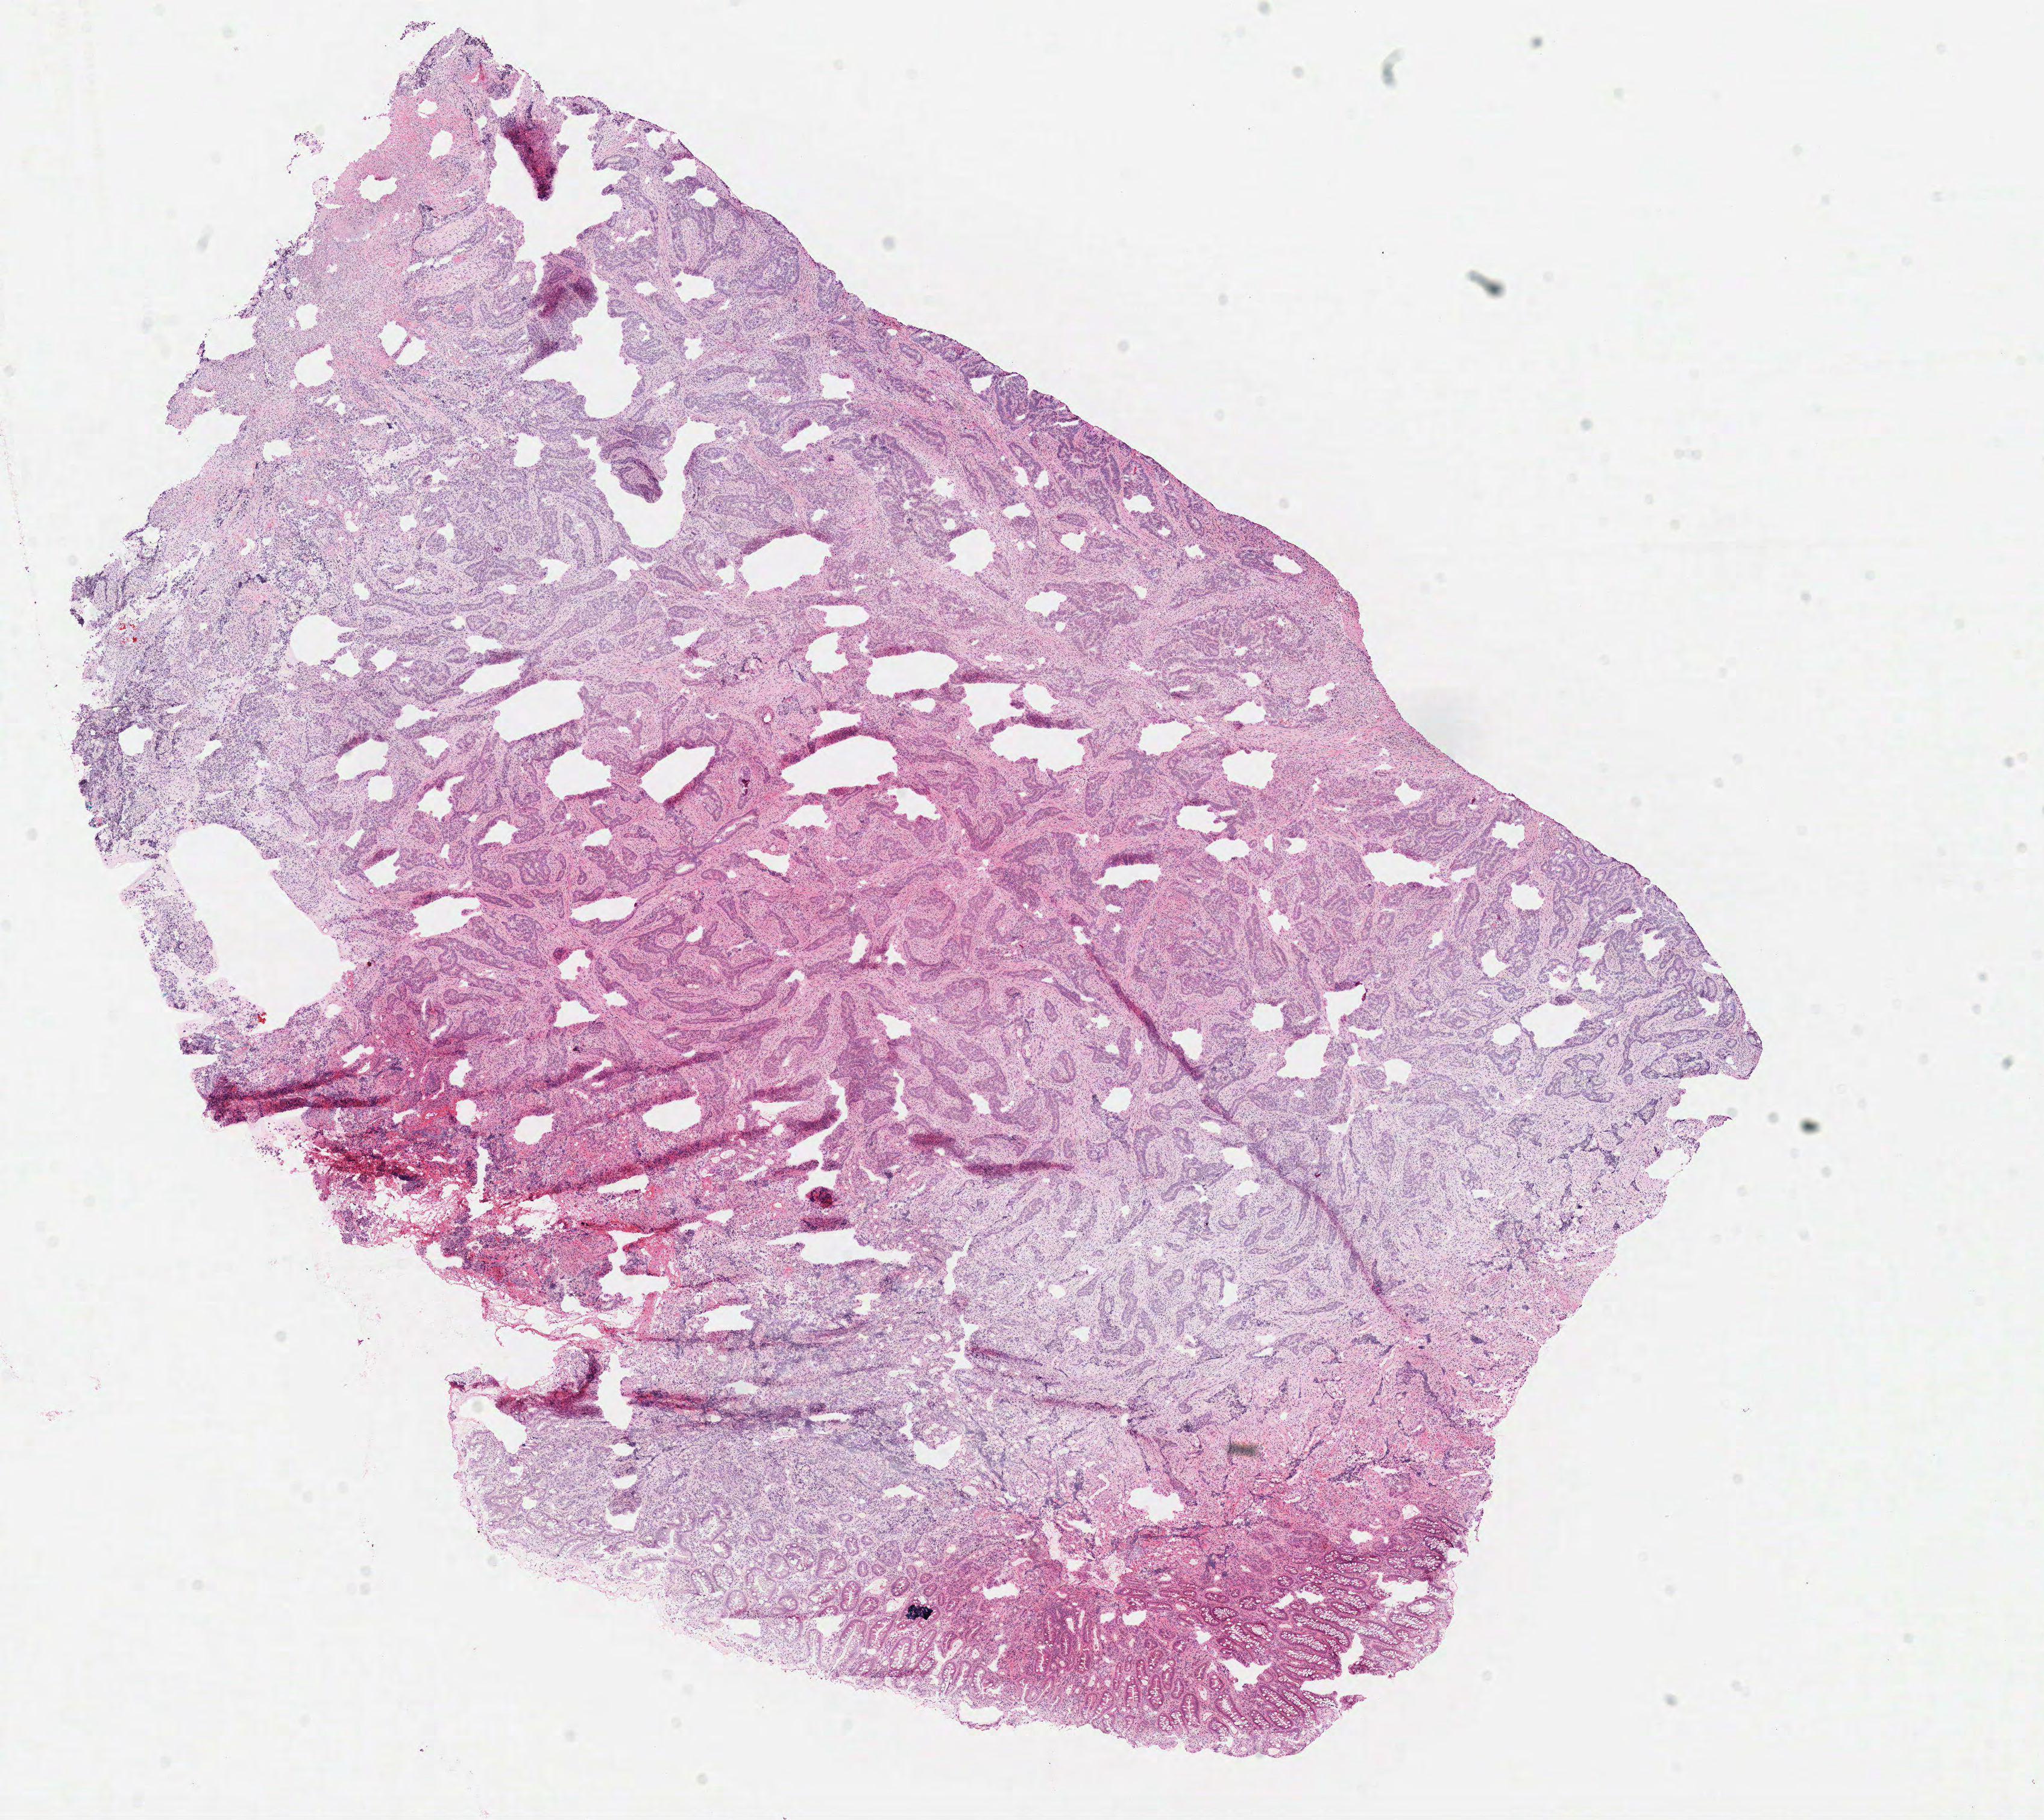
H&E whole-slide image — whole scanned area (about 13.4 x 11.9 mm) shown as a low-resolution overview; frozen section from the top of the tissue portion; rectum, primary tumour sample. Patient: male, age at initial diagnosis 70 years. Slide review estimates, as recorded: tumour cells 65%, tumour nuclei 70%, normal cells 10%, stromal cells 20%, necrosis 5%.
* lymph nodes positive (case pathology): 0 of 1 examined
* pathologic diagnosis: Adenocarcinoma, NOS
* AJCC pathologic stage: I (7th edition)